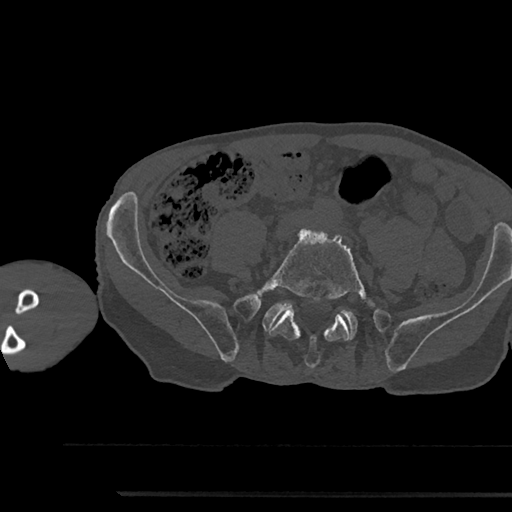
CT including the spine, one axial slice. Slice 337 of 797 in the series (ordered by position). Reconstruction kernel Br40s/3. Bone window (W 1800 / L 400 HU). 0.5 mm slice thickness. 512 × 512 image matrix, field of view 367 × 367 mm. Male patient, age 79 years. From the clinical record (not read from this slice): primary cancer: prostate.
Annotated regions visible in this slice (semi-automatic segmentation, software-assisted and operator-edited):
- L5 vertebra: box from (x=256, y=228) to (x=375, y=368) px